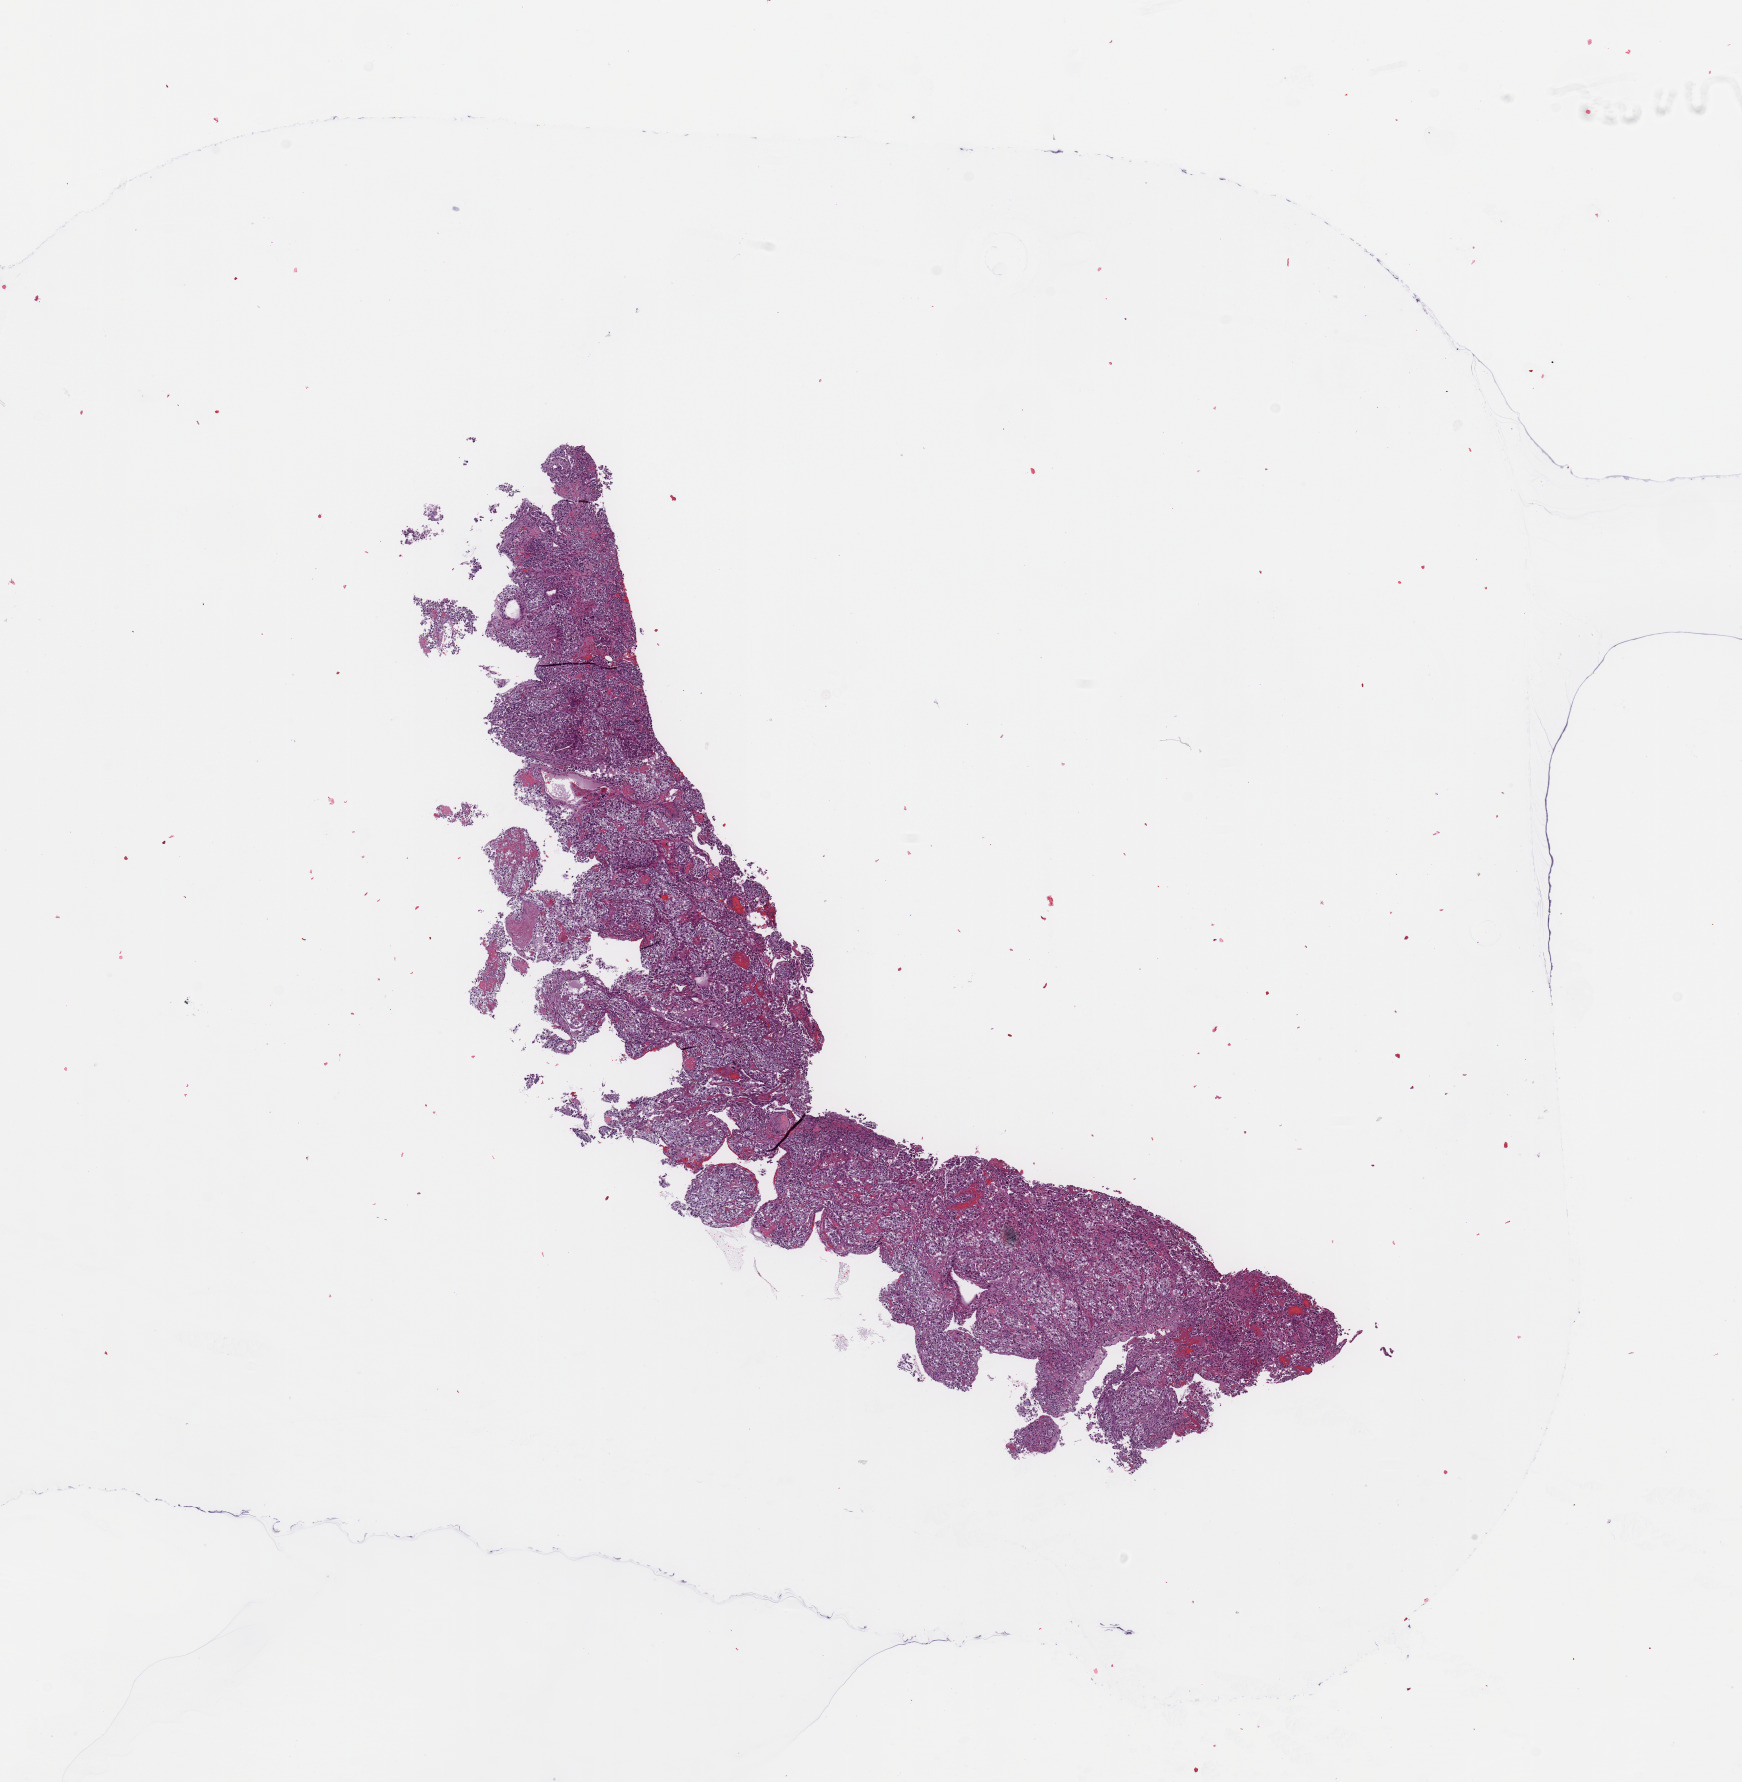
Whole-slide histology image, H&E — whole scanned area (about 13.8 x 14.1 mm, acquisition: 20x scan) shown as a low-resolution overview, tumour tissue sample, sampled site: kidney. Patient: male, age 47 years. Histologic grade: G4 (undifferentiated). Pathologist review of this section (percent, as recorded): tumour nuclei 85%, necrosis 5%.
AJCC pathologic stage: III. Primary tumour site (as recorded): lower pole. Diagnosis: Renal cell carcinoma, NOS.